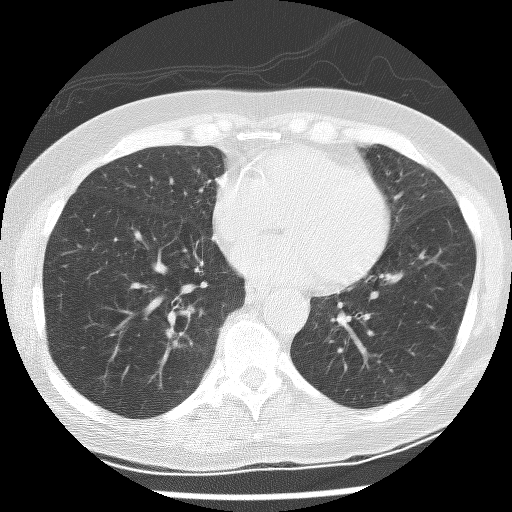
Low-dose screening chest CT, axial slice; first (baseline) screen; lung window (W 1500 / L -600 HU); lung (sharp) reconstruction kernel (BONE). Female participant, aged 60 years at enrolment. Former smoker at enrolment.
Expert reader's lesion annotation, bounding box [x1, y1, x2, y2] px = [157, 321, 203, 357]. Screening reader's record for this exam (one nodule recorded; not confirmed to be the boxed lesion): non-calcified nodule or mass ≥4 mm, right lower lobe, 10 × 6 mm, spiculated (stellate) margins, mixed attenuation. Later outcome: lung cancer diagnosed 275 days after this screen — adenocarcinoma with squamous metaplasia, right lower lobe, poorly differentiated (G3), stage IA (AJCC 6th edition), 23 mm at pathology.